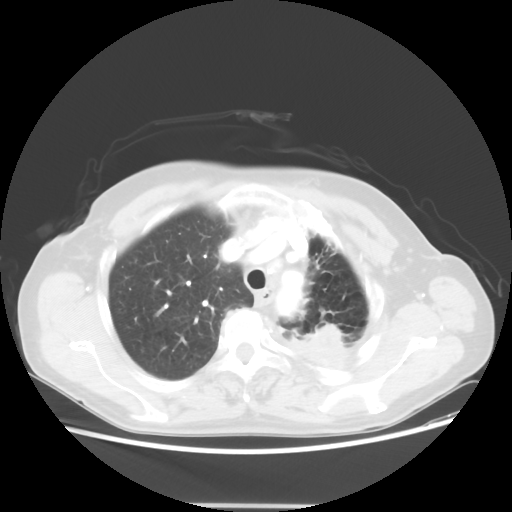
Chest CT, one axial slice; position 42 of 56 along the scan axis; reconstruction kernel STANDARD; 100 kVp; lung window (W 1500 / L -600 HU); 5 mm slice thickness; 512 × 512 image matrix, field of view 377 × 377 mm. Patient: female, 63 years. Case-level facts recorded for this patient, not image findings: clinical TNM (as recorded): T2a N0 M0.
Annotated regions visible in this slice (bounding box drawn by a radiologist):
- lung tumour (recorded histology: adenocarcinoma): box from (x=306, y=316) to (x=346, y=364) px